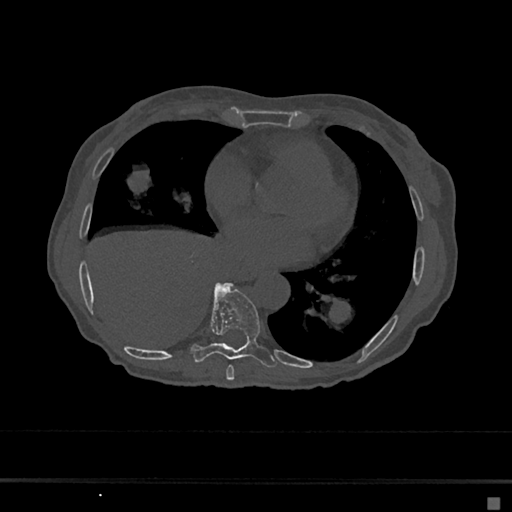
CT including the spine, one axial slice; slice 325 of 797 in the series (ordered by position); bone window (W 1800 / L 400 HU); 0.5 mm slice thickness; 512 × 512 image matrix, field of view 360 × 360 mm. Patient: female, 68 years. Case-level facts recorded for this patient, not image findings: primary cancer: renal.
Annotated regions visible in this slice (semi-automatic segmentation, software-assisted and operator-edited):
- T7 vertebra: box from (x=226, y=365) to (x=235, y=381) px
- T8 vertebra: (x=191, y=282)–(x=277, y=368)